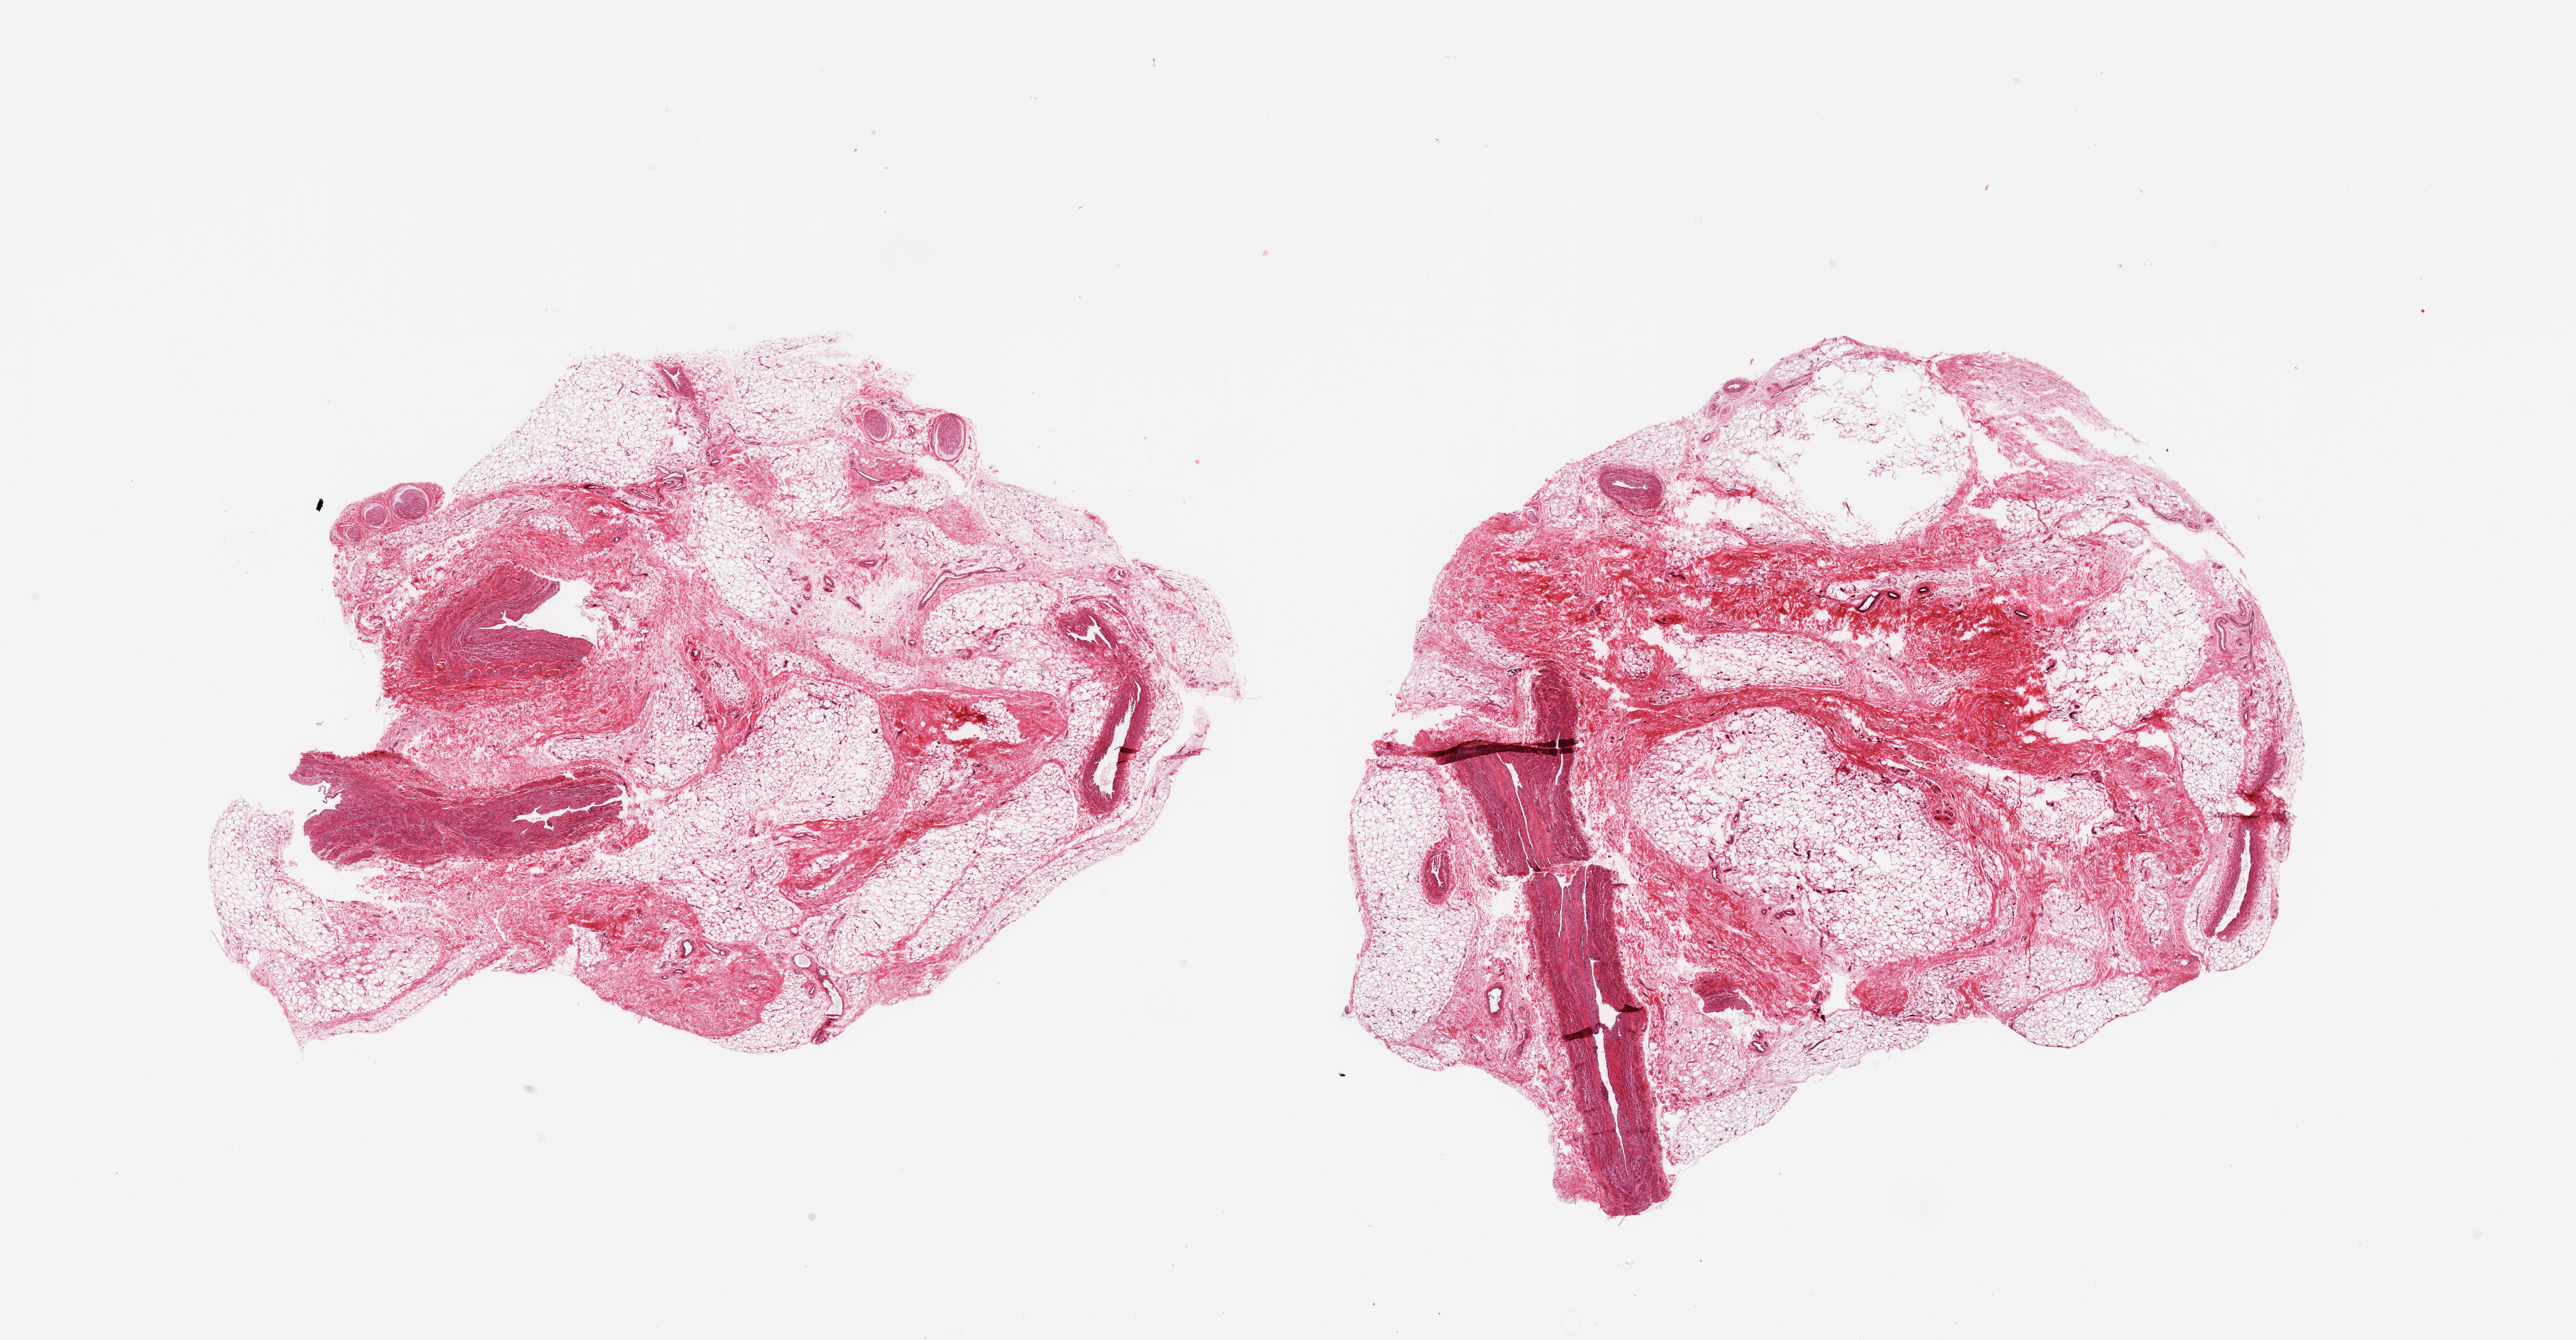
Digitized haematoxylin and eosin-stained section — shown as a low-resolution overview of the whole scanned area (about 30.5 x 15.9 mm); PAXgene-fixed paraffin-embedded (PFPE) section; target tissue: adipose tissue; donor tissue sample.
Pathologist's review note for this sample: 2 pieces; adipose tissue with ~40% large vessels/nerve.